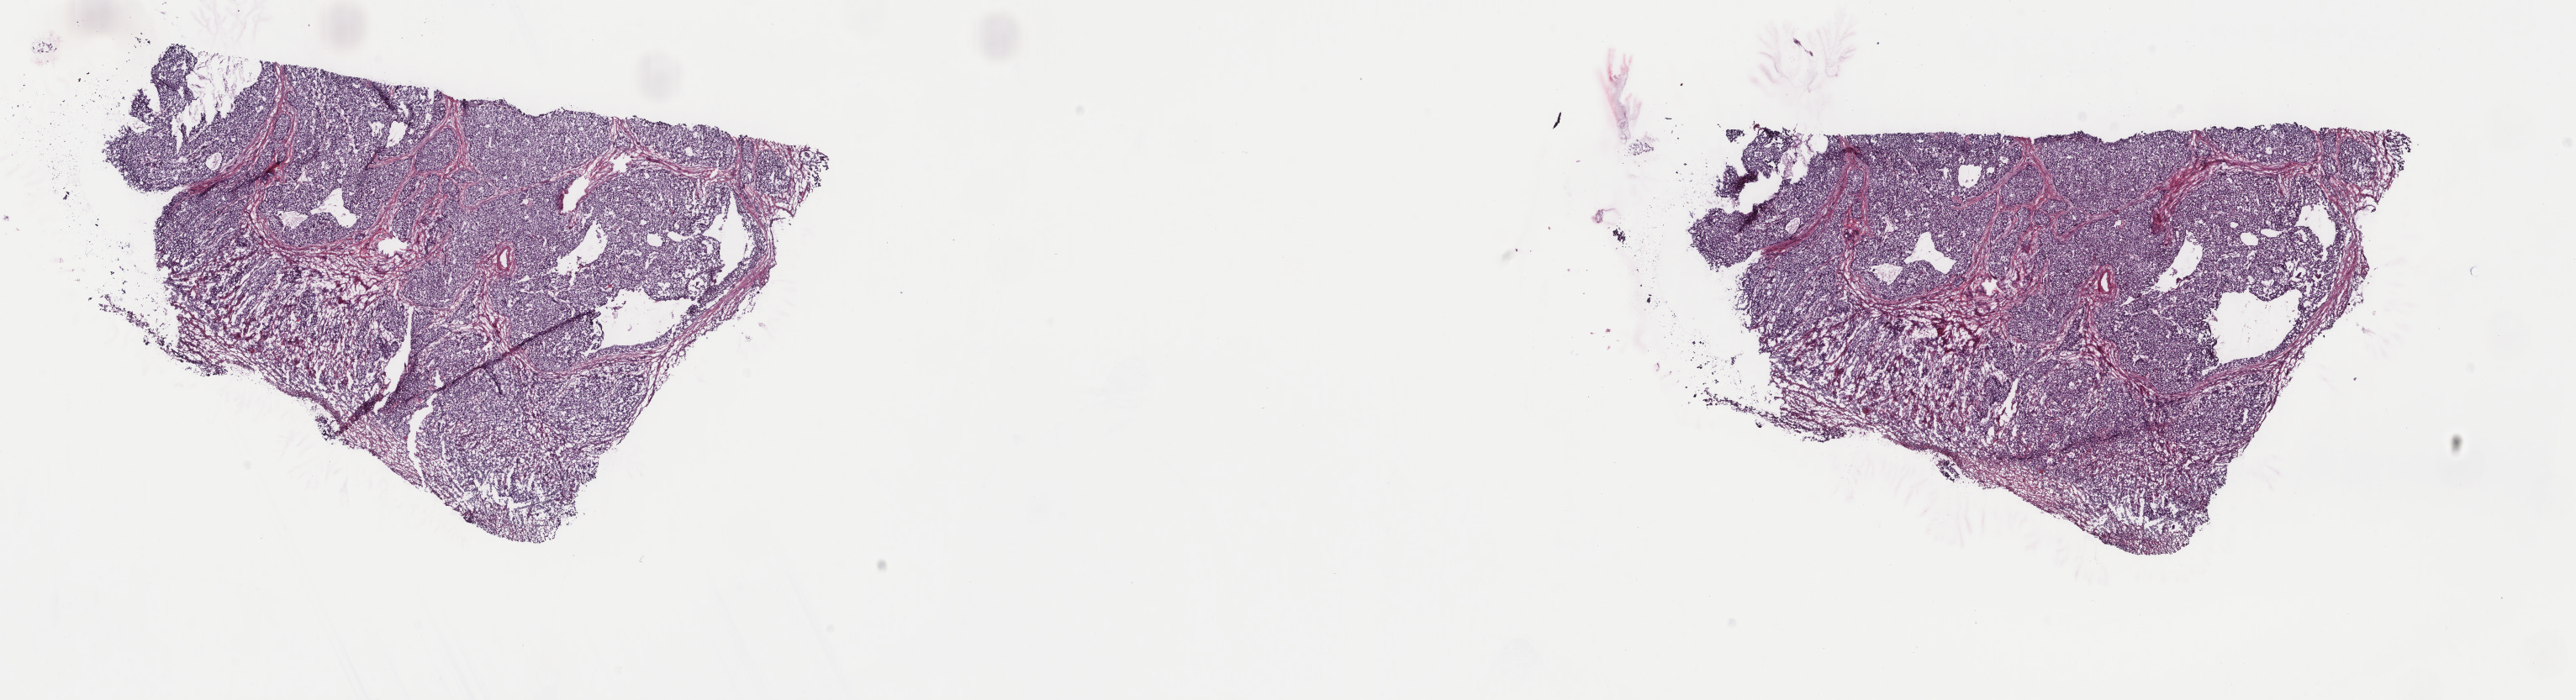
H&E-stained whole-slide image — shown as a low-resolution overview of the whole scanned area (about 24.3 x 6.6 mm), frozen section from the top of the tissue portion, sample: primary tumour, stomach. Male patient; age at initial diagnosis 77 years. Histologic grade: G3 (poorly differentiated). Pathologist review of this section (percent, as recorded): tumour cells 78%, tumour nuclei 90%, normal cells 0%, stromal cells 18%, necrosis 4%. Infiltration values recorded for this section: lymphocyte infiltration 2%, monocyte infiltration 0%, neutrophil infiltration 1%.
Lymph nodes positive (case pathology): 7 of 15 examined. AJCC pathologic stage: IIIC (7th edition). Diagnosis: Adenocarcinoma, NOS (fundus of stomach).